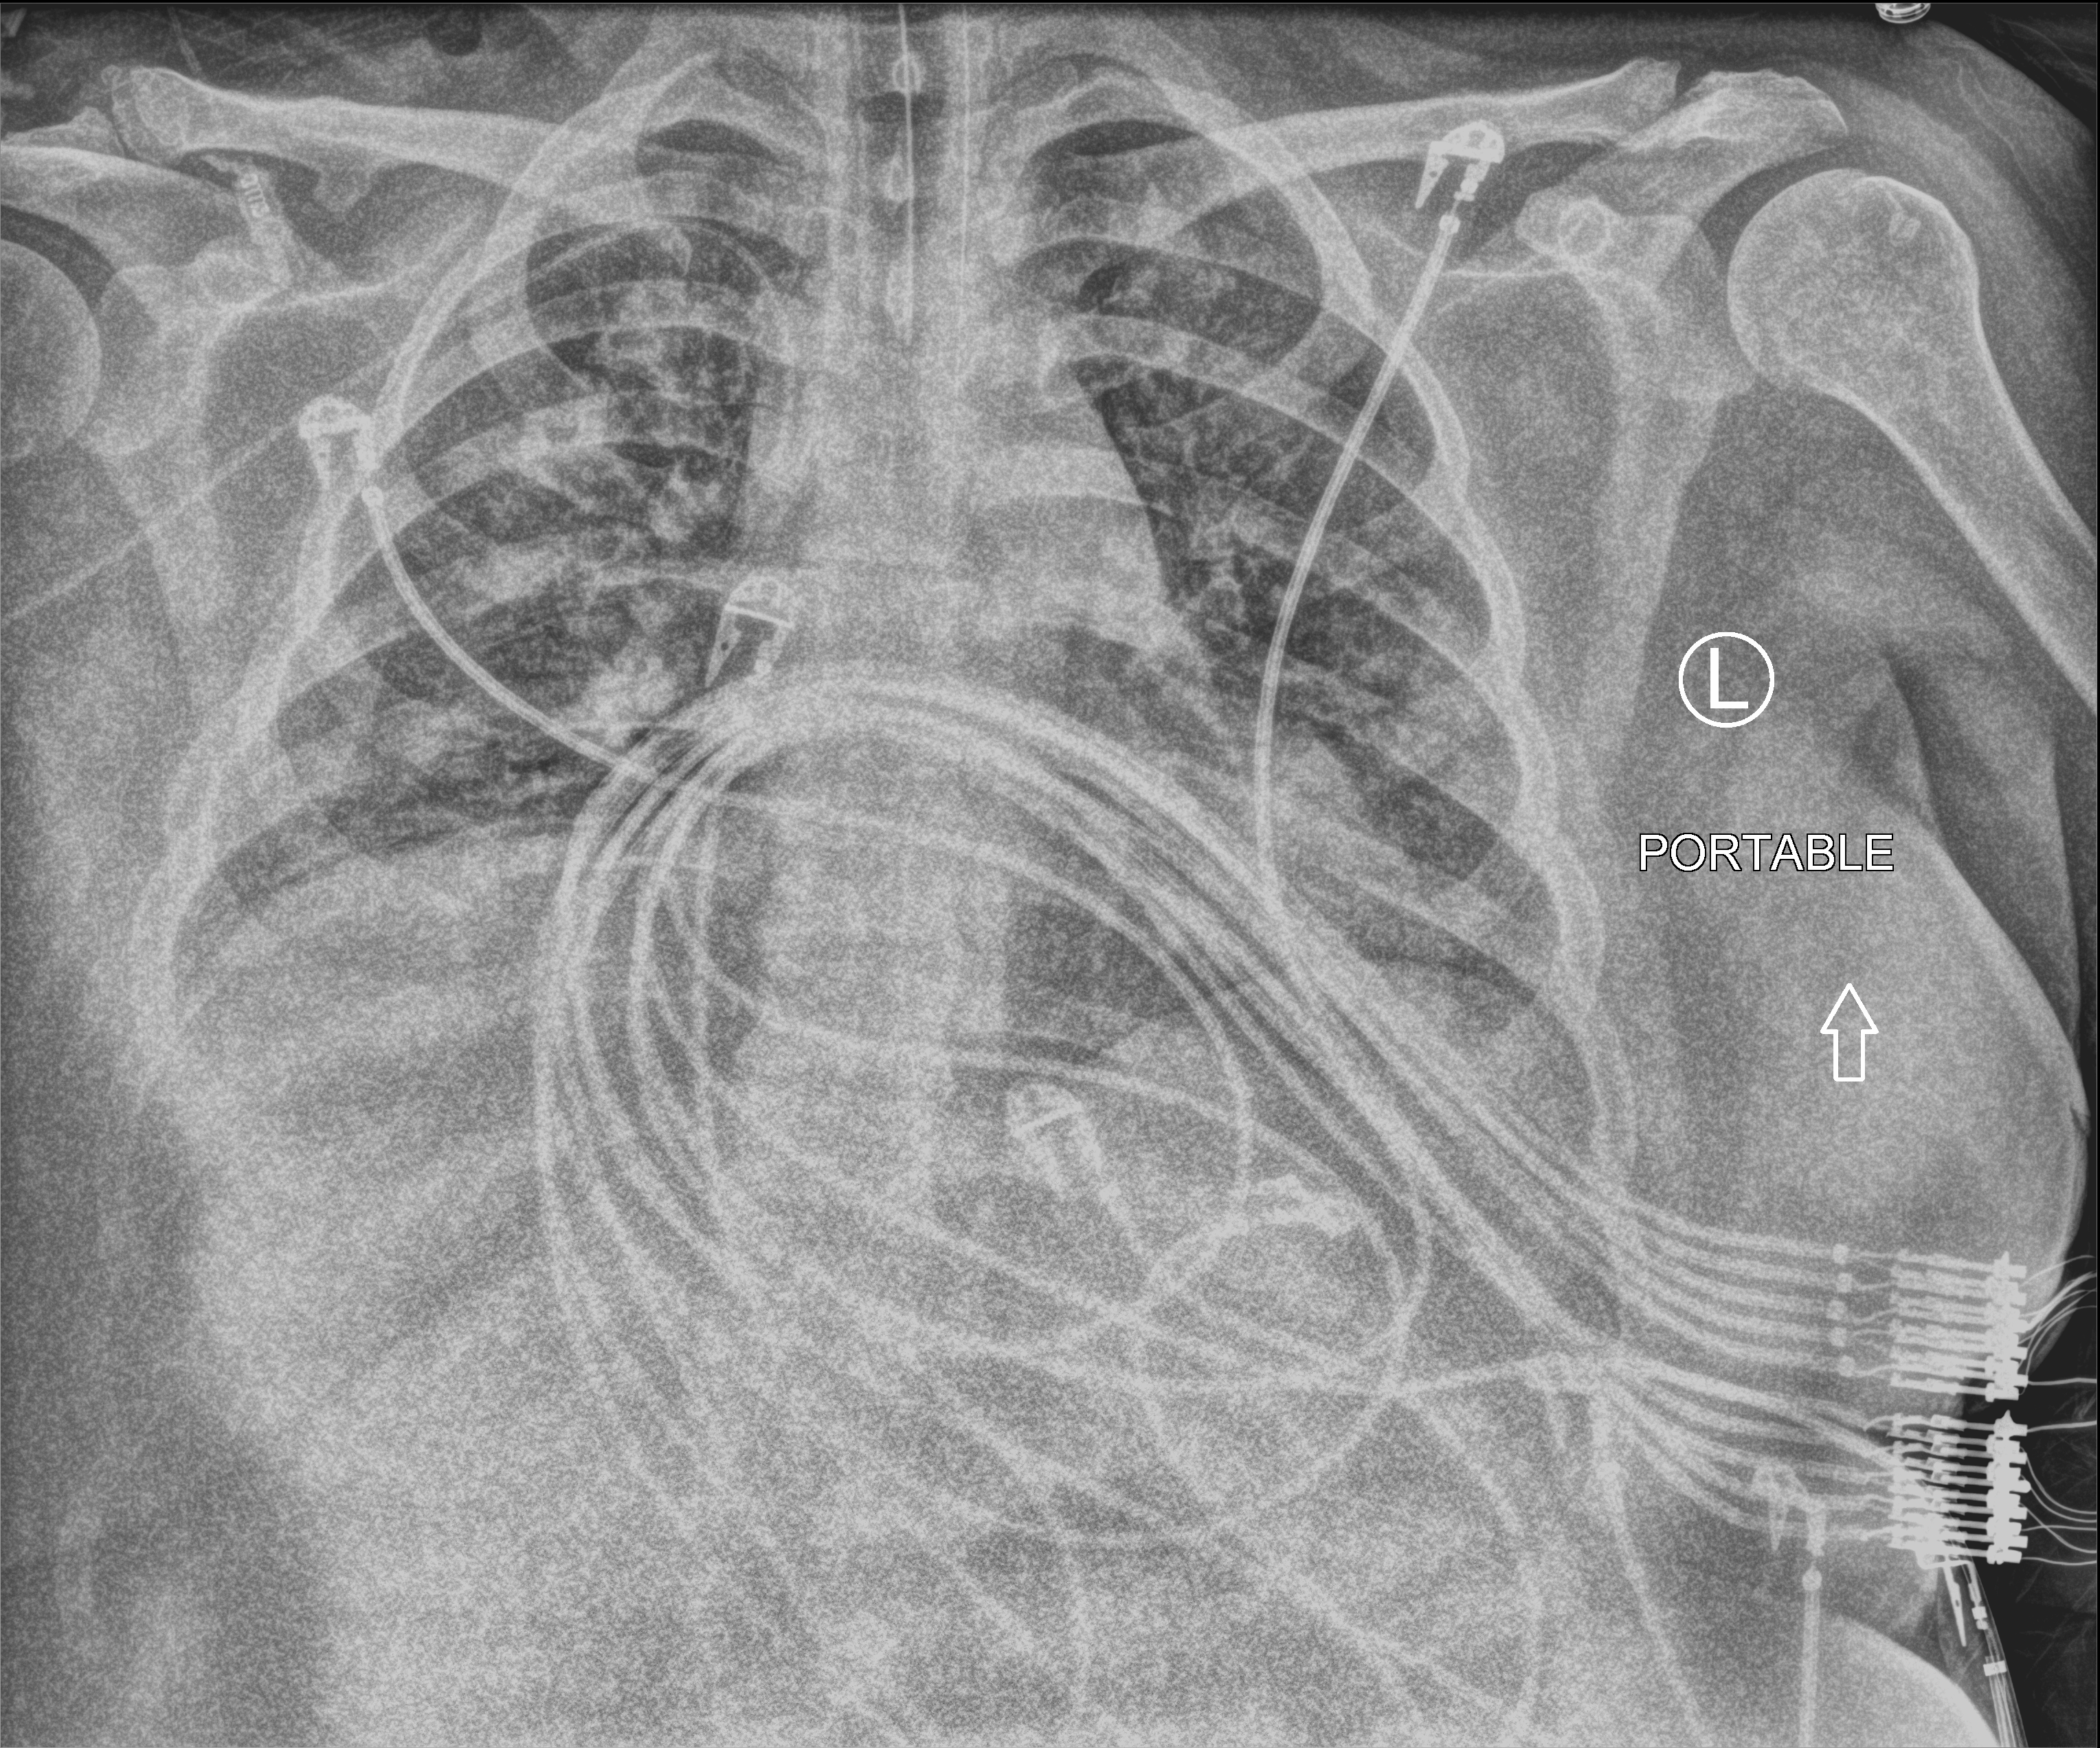
Bedside chest radiograph (computed radiography), anteroposterior (AP) projection. Patient hospitalised with COVID-19; female, aged 18–59 years.
From the hospital-stay record, not from the radiograph (when in the stay this image was taken is not recorded): admitted to intensive care during this hospital stay: yes.